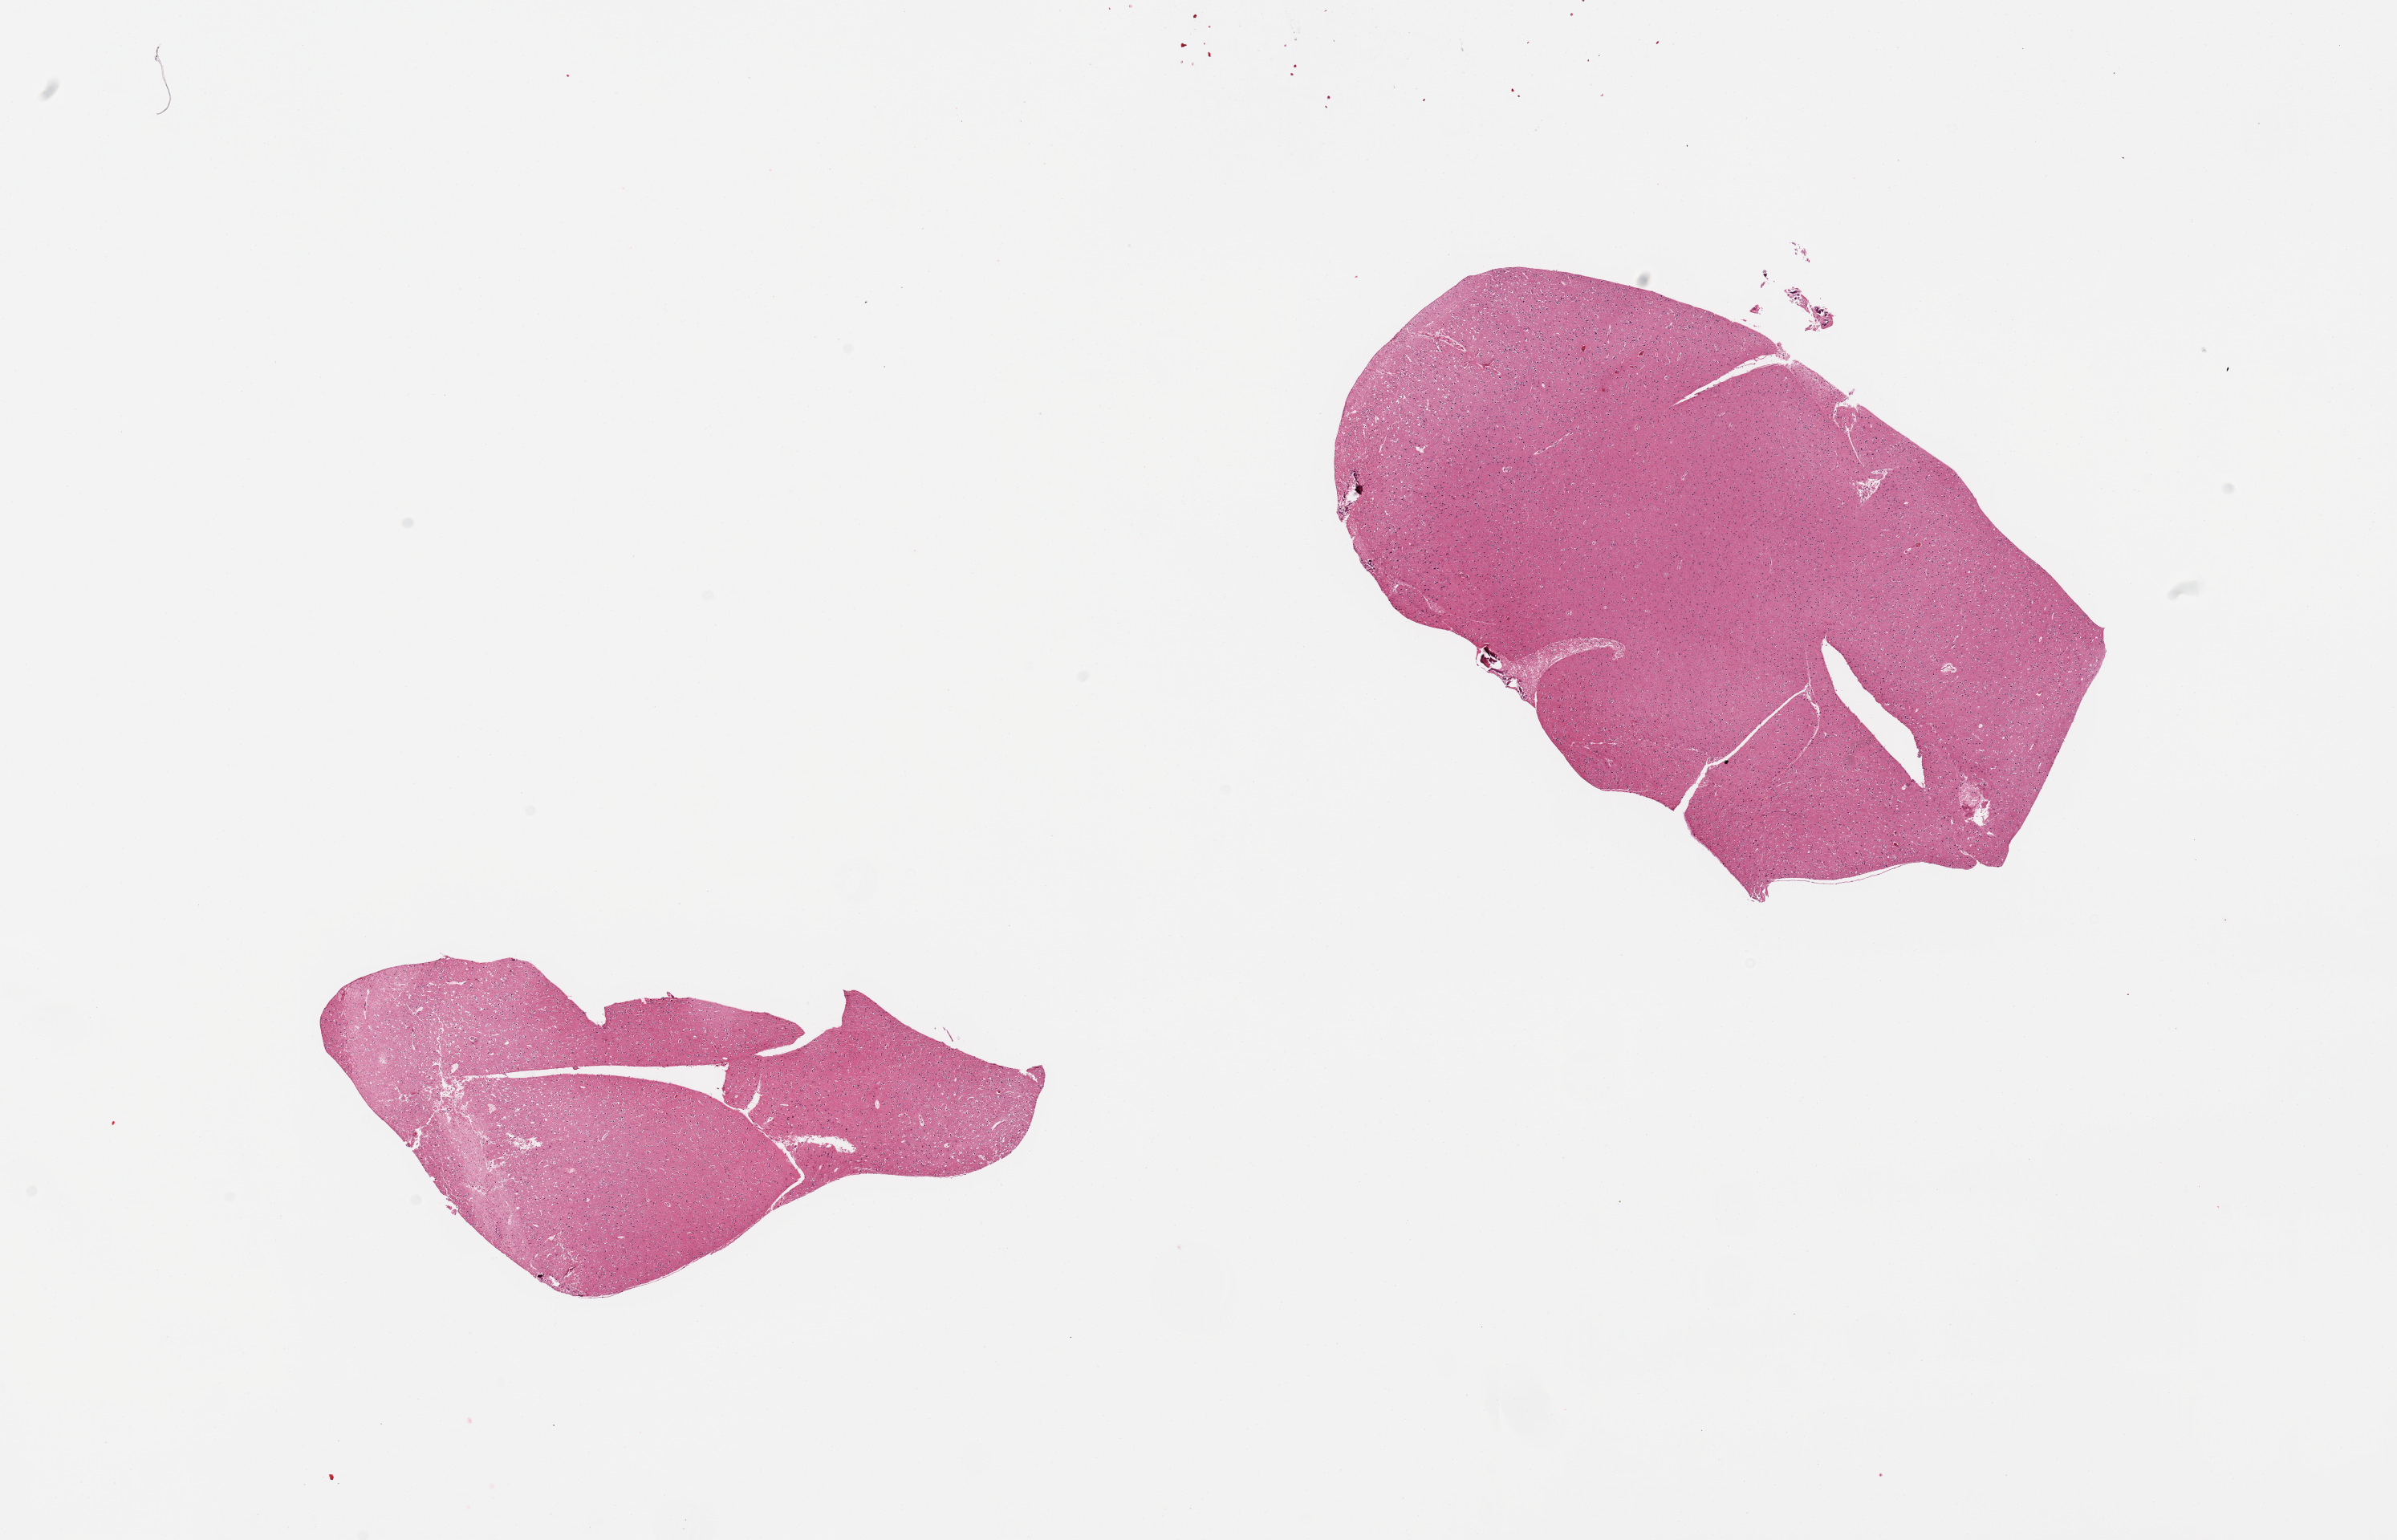
Whole-slide image, H&E stain, a low-resolution overview of the entire scanned area, about 23.6 x 15.2 mm. PAXgene-fixed, paraffin-embedded tissue. Sampled site (target tissue): cerebral cortex. Donor tissue sample.
Reviewer comment on this tissue sample: 2 pieces, no abnormalities.